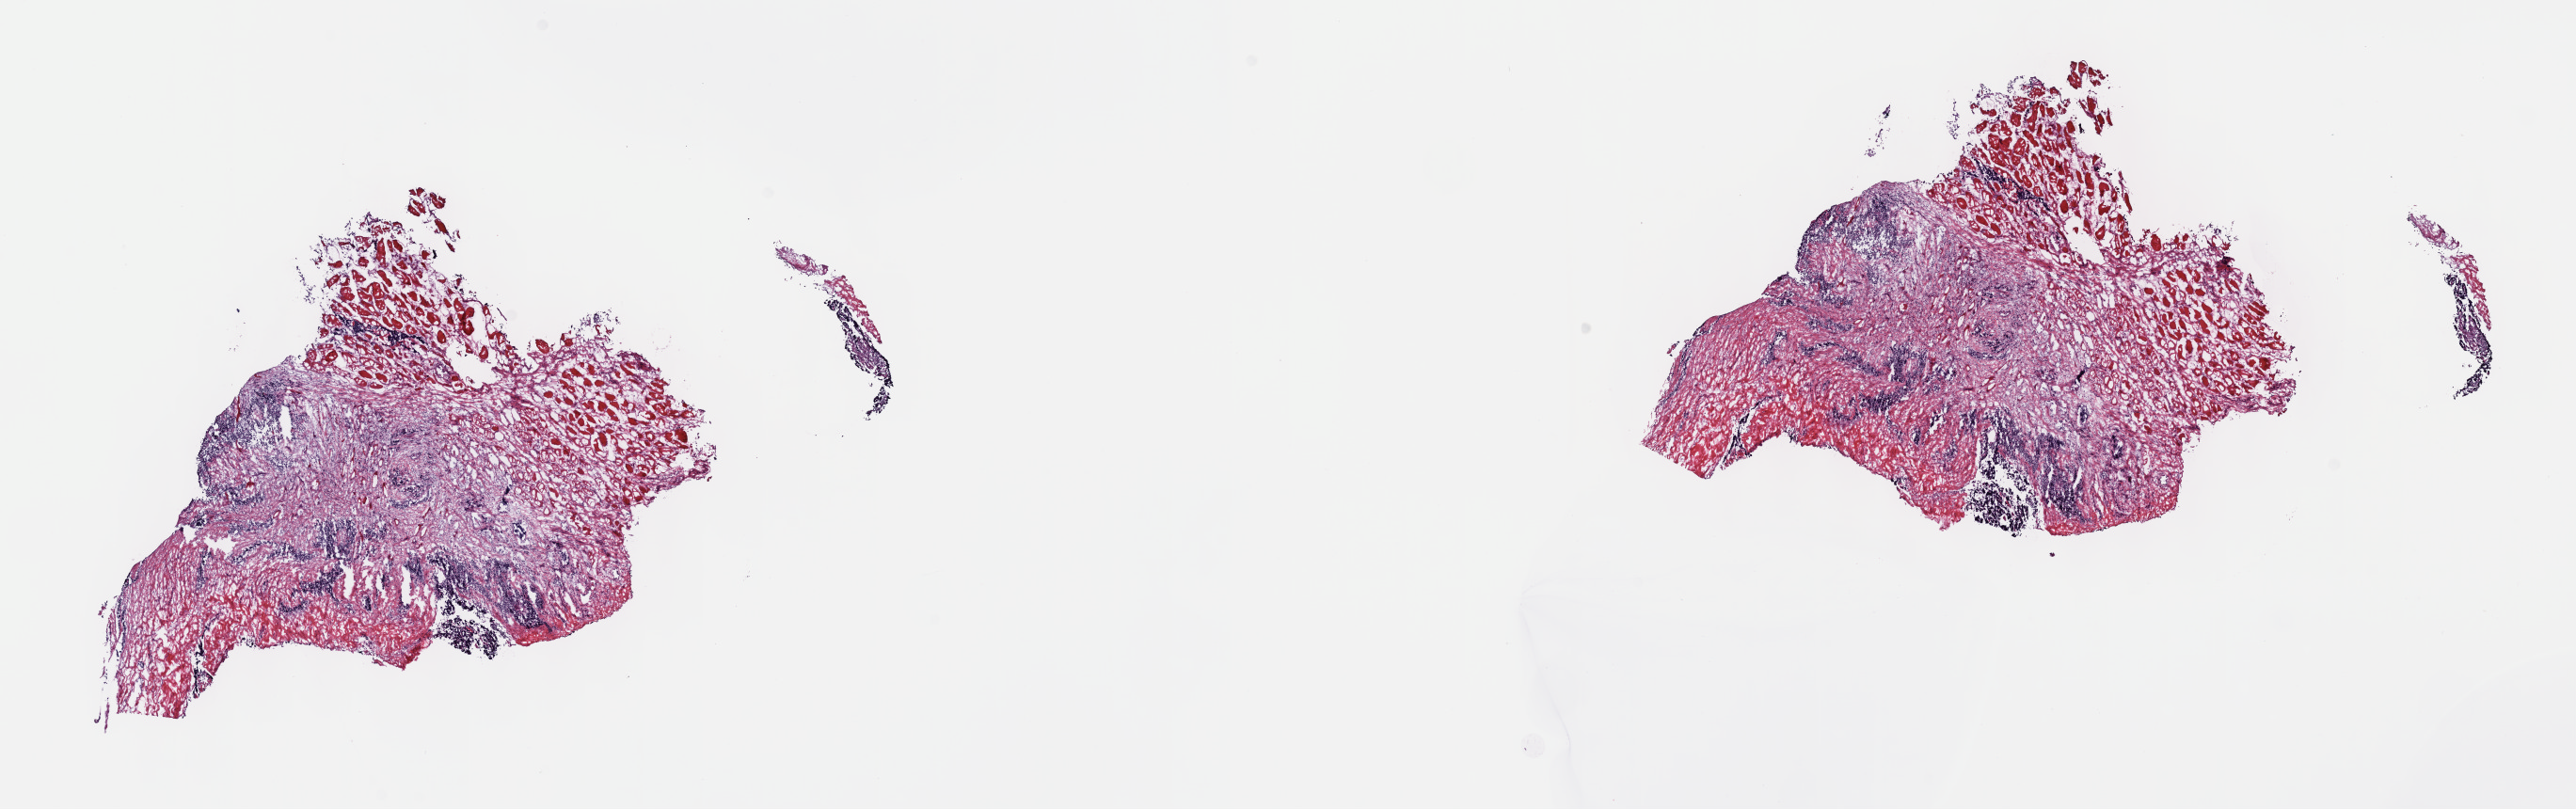
H&E-stained whole-slide image — low-resolution overview of the scanned area, about 22.1 x 7.0 mm. Frozen section. Primary tumour sample from the connective, subcutaneous and other soft tissues. Patient: female, age at initial diagnosis 35 years. Composition of this section per pathologist review: tumour cells 25%, tumour nuclei 60%, normal cells 45%, stromal cells 30%, necrosis 0%. Inflammatory infiltration, as recorded: lymphocyte infiltration 2%, monocyte infiltration 4%, neutrophil infiltration 0%.
Histologic diagnosis: Synovial sarcoma, NOS (connective, subcutaneous and other soft tissues of upper limb and shoulder).